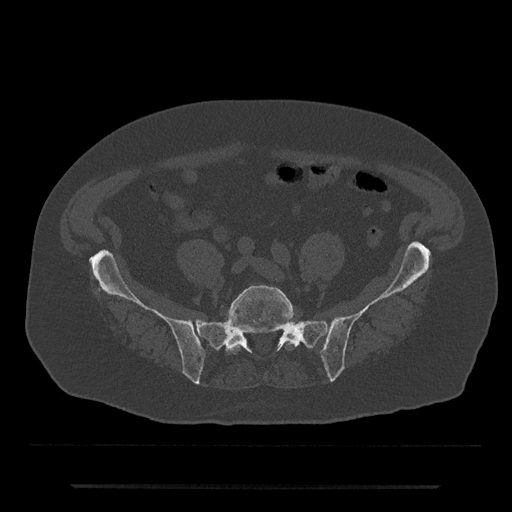
CT including the spine, one axial slice; position 259 of 797 along the scan axis; reconstruction kernel Br40s/3; 120 kVp; bone window (W 1800 / L 400 HU); 0.5 mm slice thickness; 512 × 512 image matrix, field of view 434 × 434 mm. Patient: male, 80 years. From the clinical record (not read from this slice): primary cancer: prostate.
Outlined on this slice (semi-automatic segmentation, software-assisted and operator-edited):
- L5 vertebra: box from (x=225, y=285) to (x=296, y=355) px